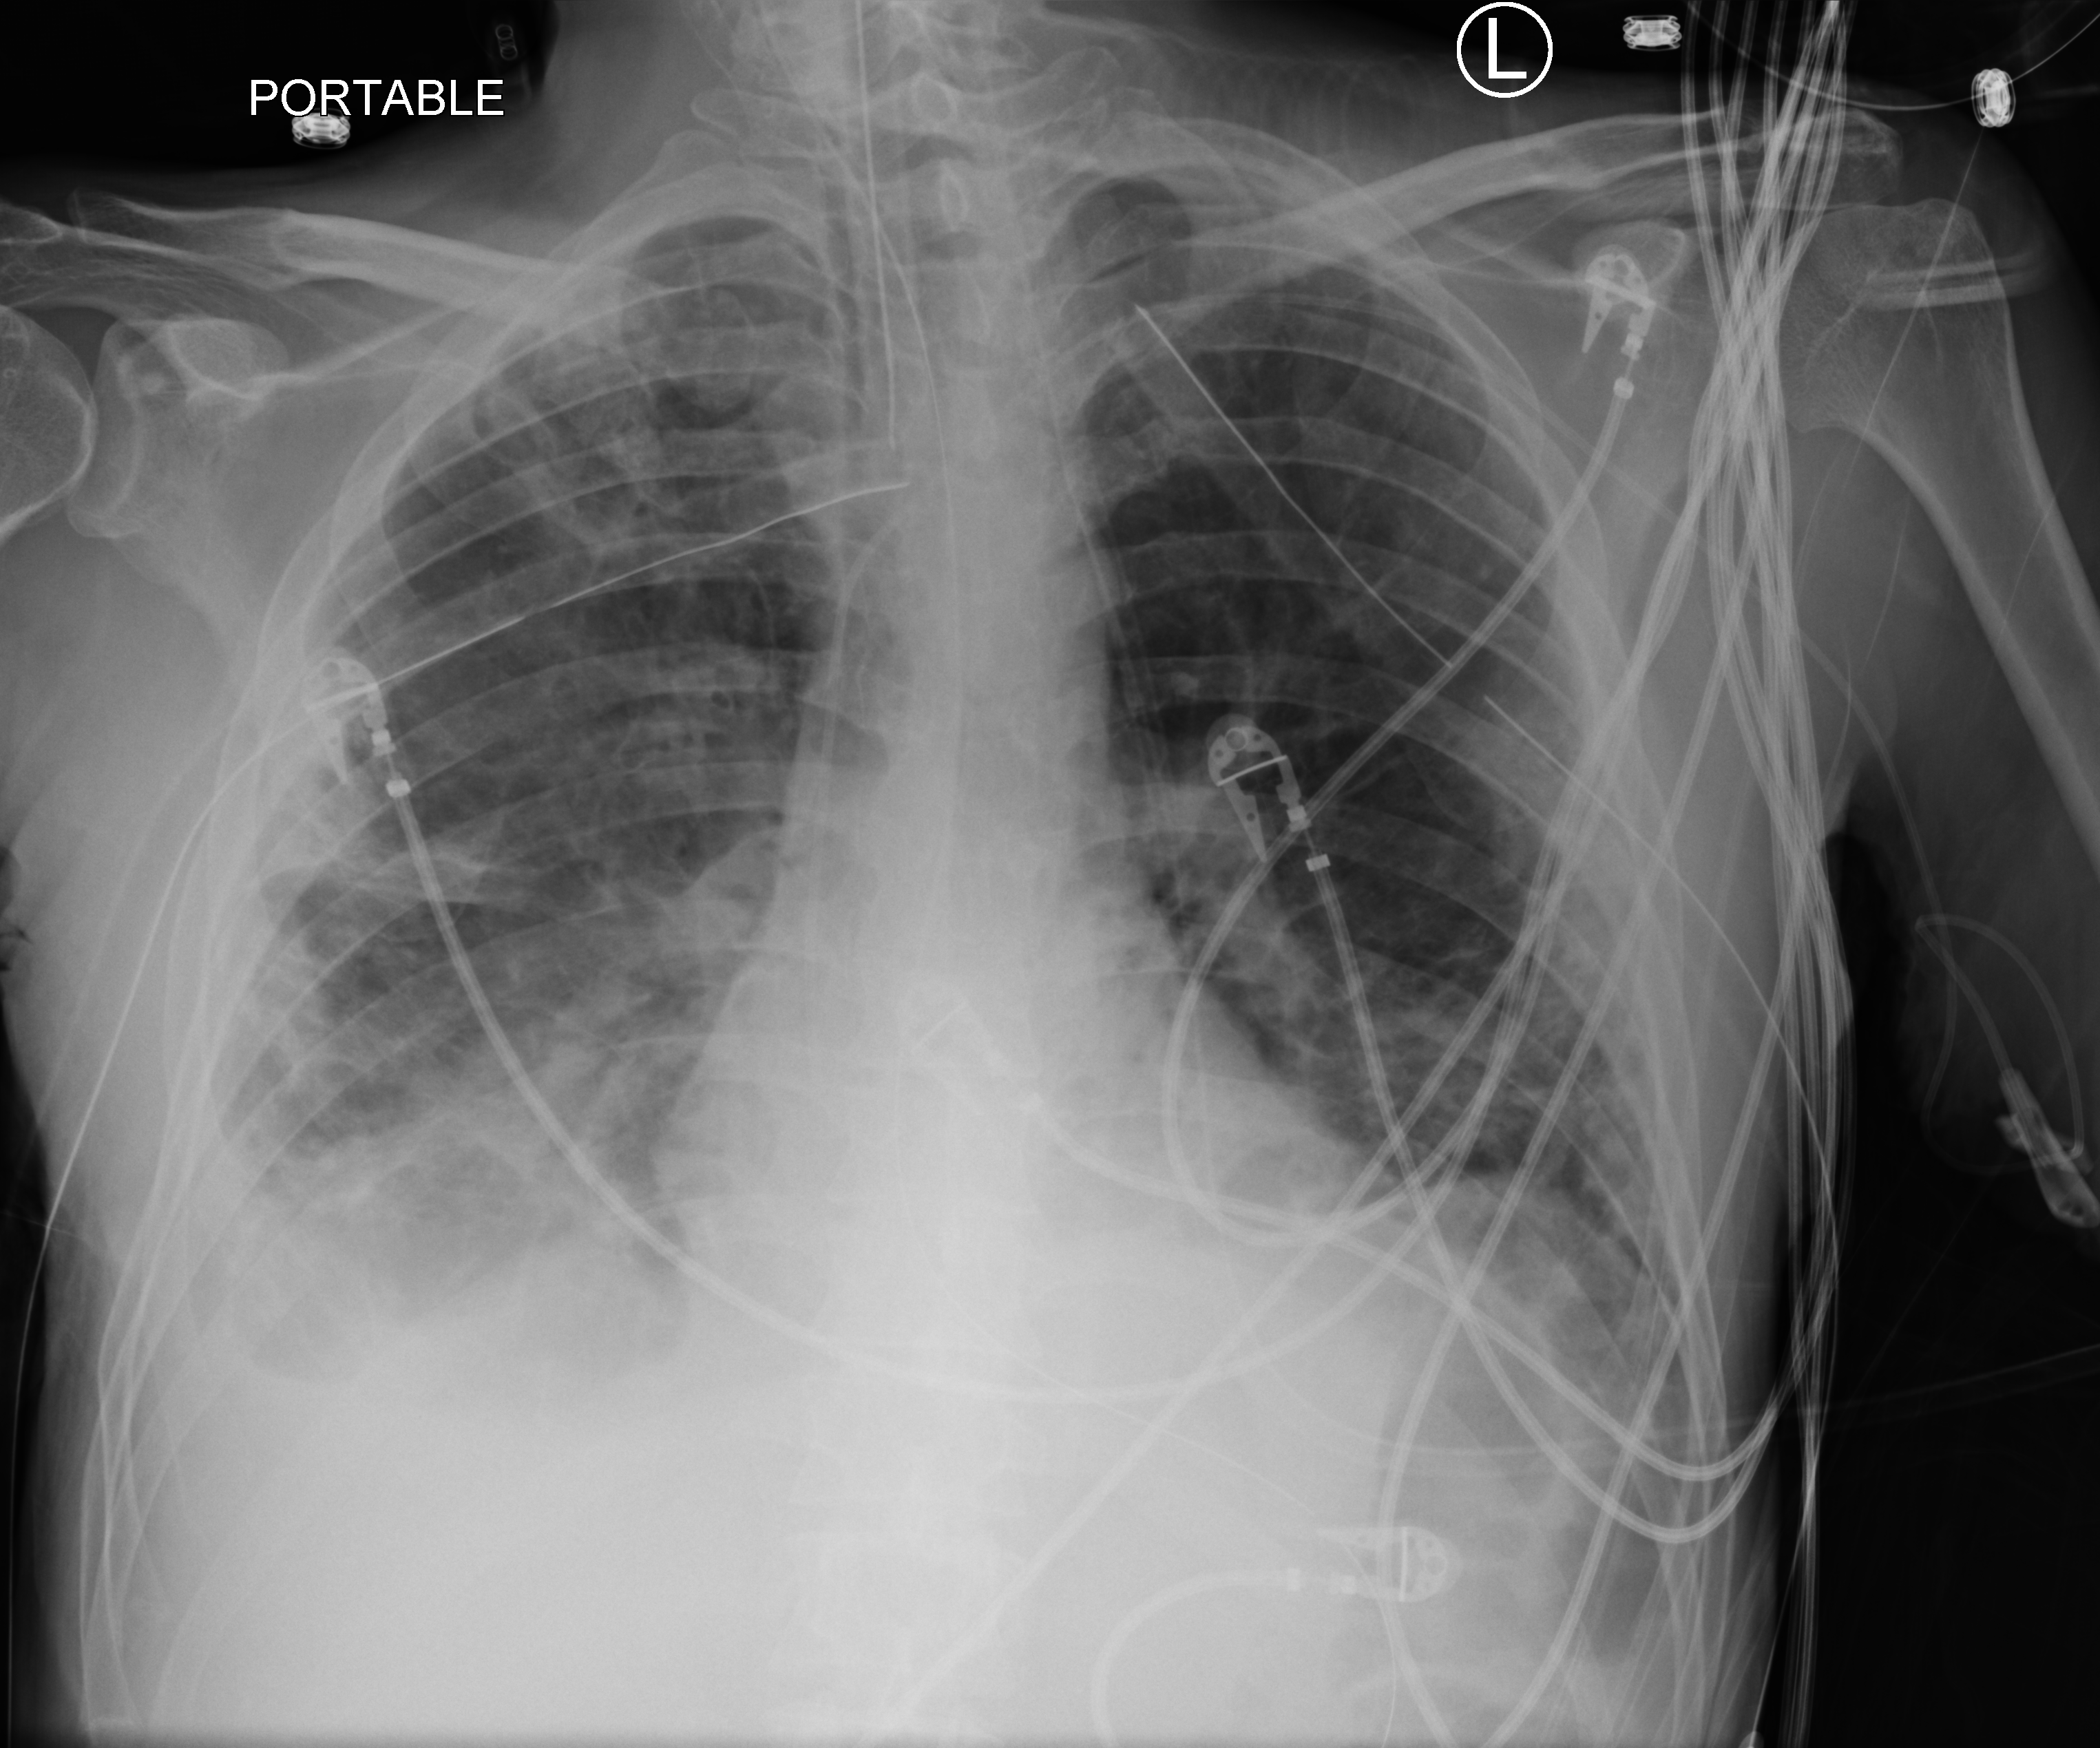
Chest X-ray (portable); anteroposterior (AP) projection. Male patient hospitalised with COVID-19, age 18–59 years.
From the hospital-stay record, not from the radiograph (when in the stay this image was taken is not recorded):
- mechanically ventilated during this hospital stay: yes
- admitted to intensive care during this hospital stay: yes
- other chronic lung disease (admission record): no